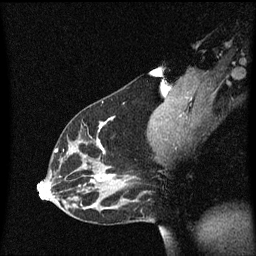
Breast MRI (dynamic contrast-enhanced), one sagittal slice. Position 33 of 60 along the scan axis. Dynamic contrast-enhanced series, image 2 of 3 at this slice position (ordered by acquisition). 1.5 T. TE 4.2 ms, TR 8.4 ms. 2 mm slice thickness. 256 × 256 image matrix, field of view 200 × 200 mm. Female patient, age 33 years.
Outlined on this slice (semi-automatically segmented with operator editing):
- analysis volume of interest (the breast-tissue region the enhancement analysis was run in; not a lesion): bounding box (x1, y1, x2, y2) in pixels: (45, 114, 152, 191)
- tumour enhancement mask (voxels above the 70 % enhancement threshold inside the analysis volume of interest): (56, 118, 117, 187)